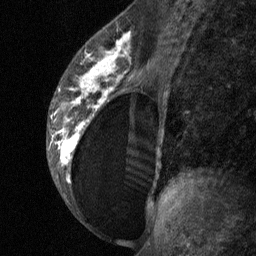
Breast MRI (dynamic contrast-enhanced), one sagittal slice; dynamic contrast-enhanced study with each time point stored as its own series, time point 2 of 3 at this slice position (early post-contrast, ordered by acquisition time); 1.5 T; TE 4.8 ms, TR 27 ms; 2 mm slice thickness; 256 × 256 image matrix, field of view 180 × 180 mm. Patient: female, 34 years. From the clinical record (not read from this slice): setting: breast cancer imaged before/during neoadjuvant chemotherapy; receptor status: HR-positive, HER2-negative.
Annotated regions visible in this slice (semi-automatically segmented with operator editing):
- analysis volume of interest (the breast-tissue region the enhancement analysis was run in; not a lesion): bounding box (x1, y1, x2, y2) in pixels: (46, 23, 157, 197)
- tumour enhancement mask (voxels above the 90 % enhancement threshold inside the analysis volume of interest): (53, 33, 130, 181)